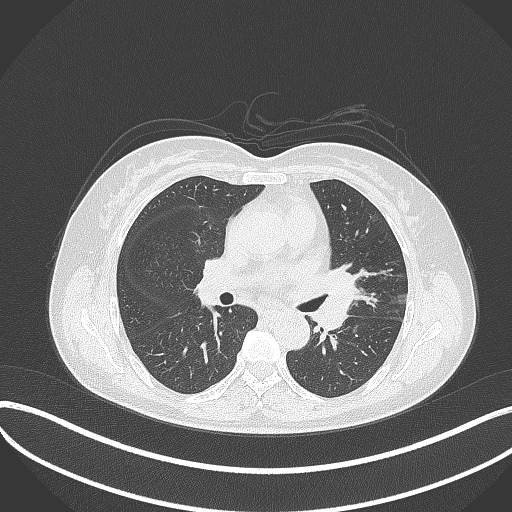
Chest CT, one axial slice; position 194 of 373 along the scan axis; reconstruction kernel B70f; 120 kVp; lung window (W 1500 / L -600 HU); 1 mm slice thickness; 512 × 512 image matrix, field of view 400 × 400 mm. Female patient, age 54 years. From the clinical record (not read from this slice): clinical TNM (as recorded): T2a N1 M0.
Annotated regions visible in this slice (bounding box drawn by a radiologist):
- lung tumour (recorded histology: small cell carcinoma): bounding box <316,266,359,330> (left, top, right, bottom; pixels)